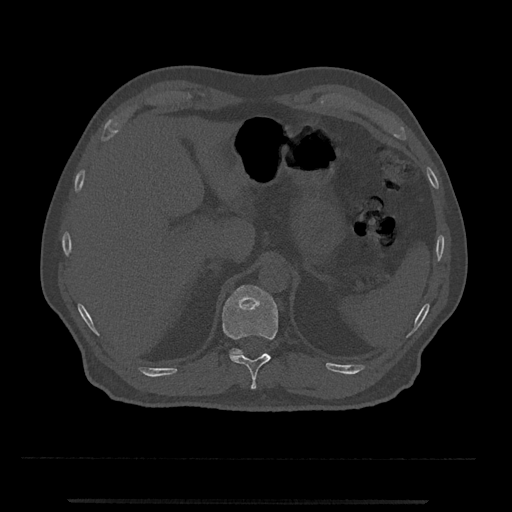
CT including the spine, one axial slice. Position 451 of 797 along the scan axis. 120 kVp. Bone window (W 1800 / L 400 HU). 512 × 512 image matrix. Patient: male, 63 years. Case-level facts recorded for this patient, not image findings: primary cancer: prostate.
Annotated regions visible in this slice (semi-automatically segmented with operator editing):
- T11 vertebra: bounding box (x1, y1, x2, y2) in pixels: (222, 285, 278, 390)
- T12 vertebra: (230, 348, 267, 356)